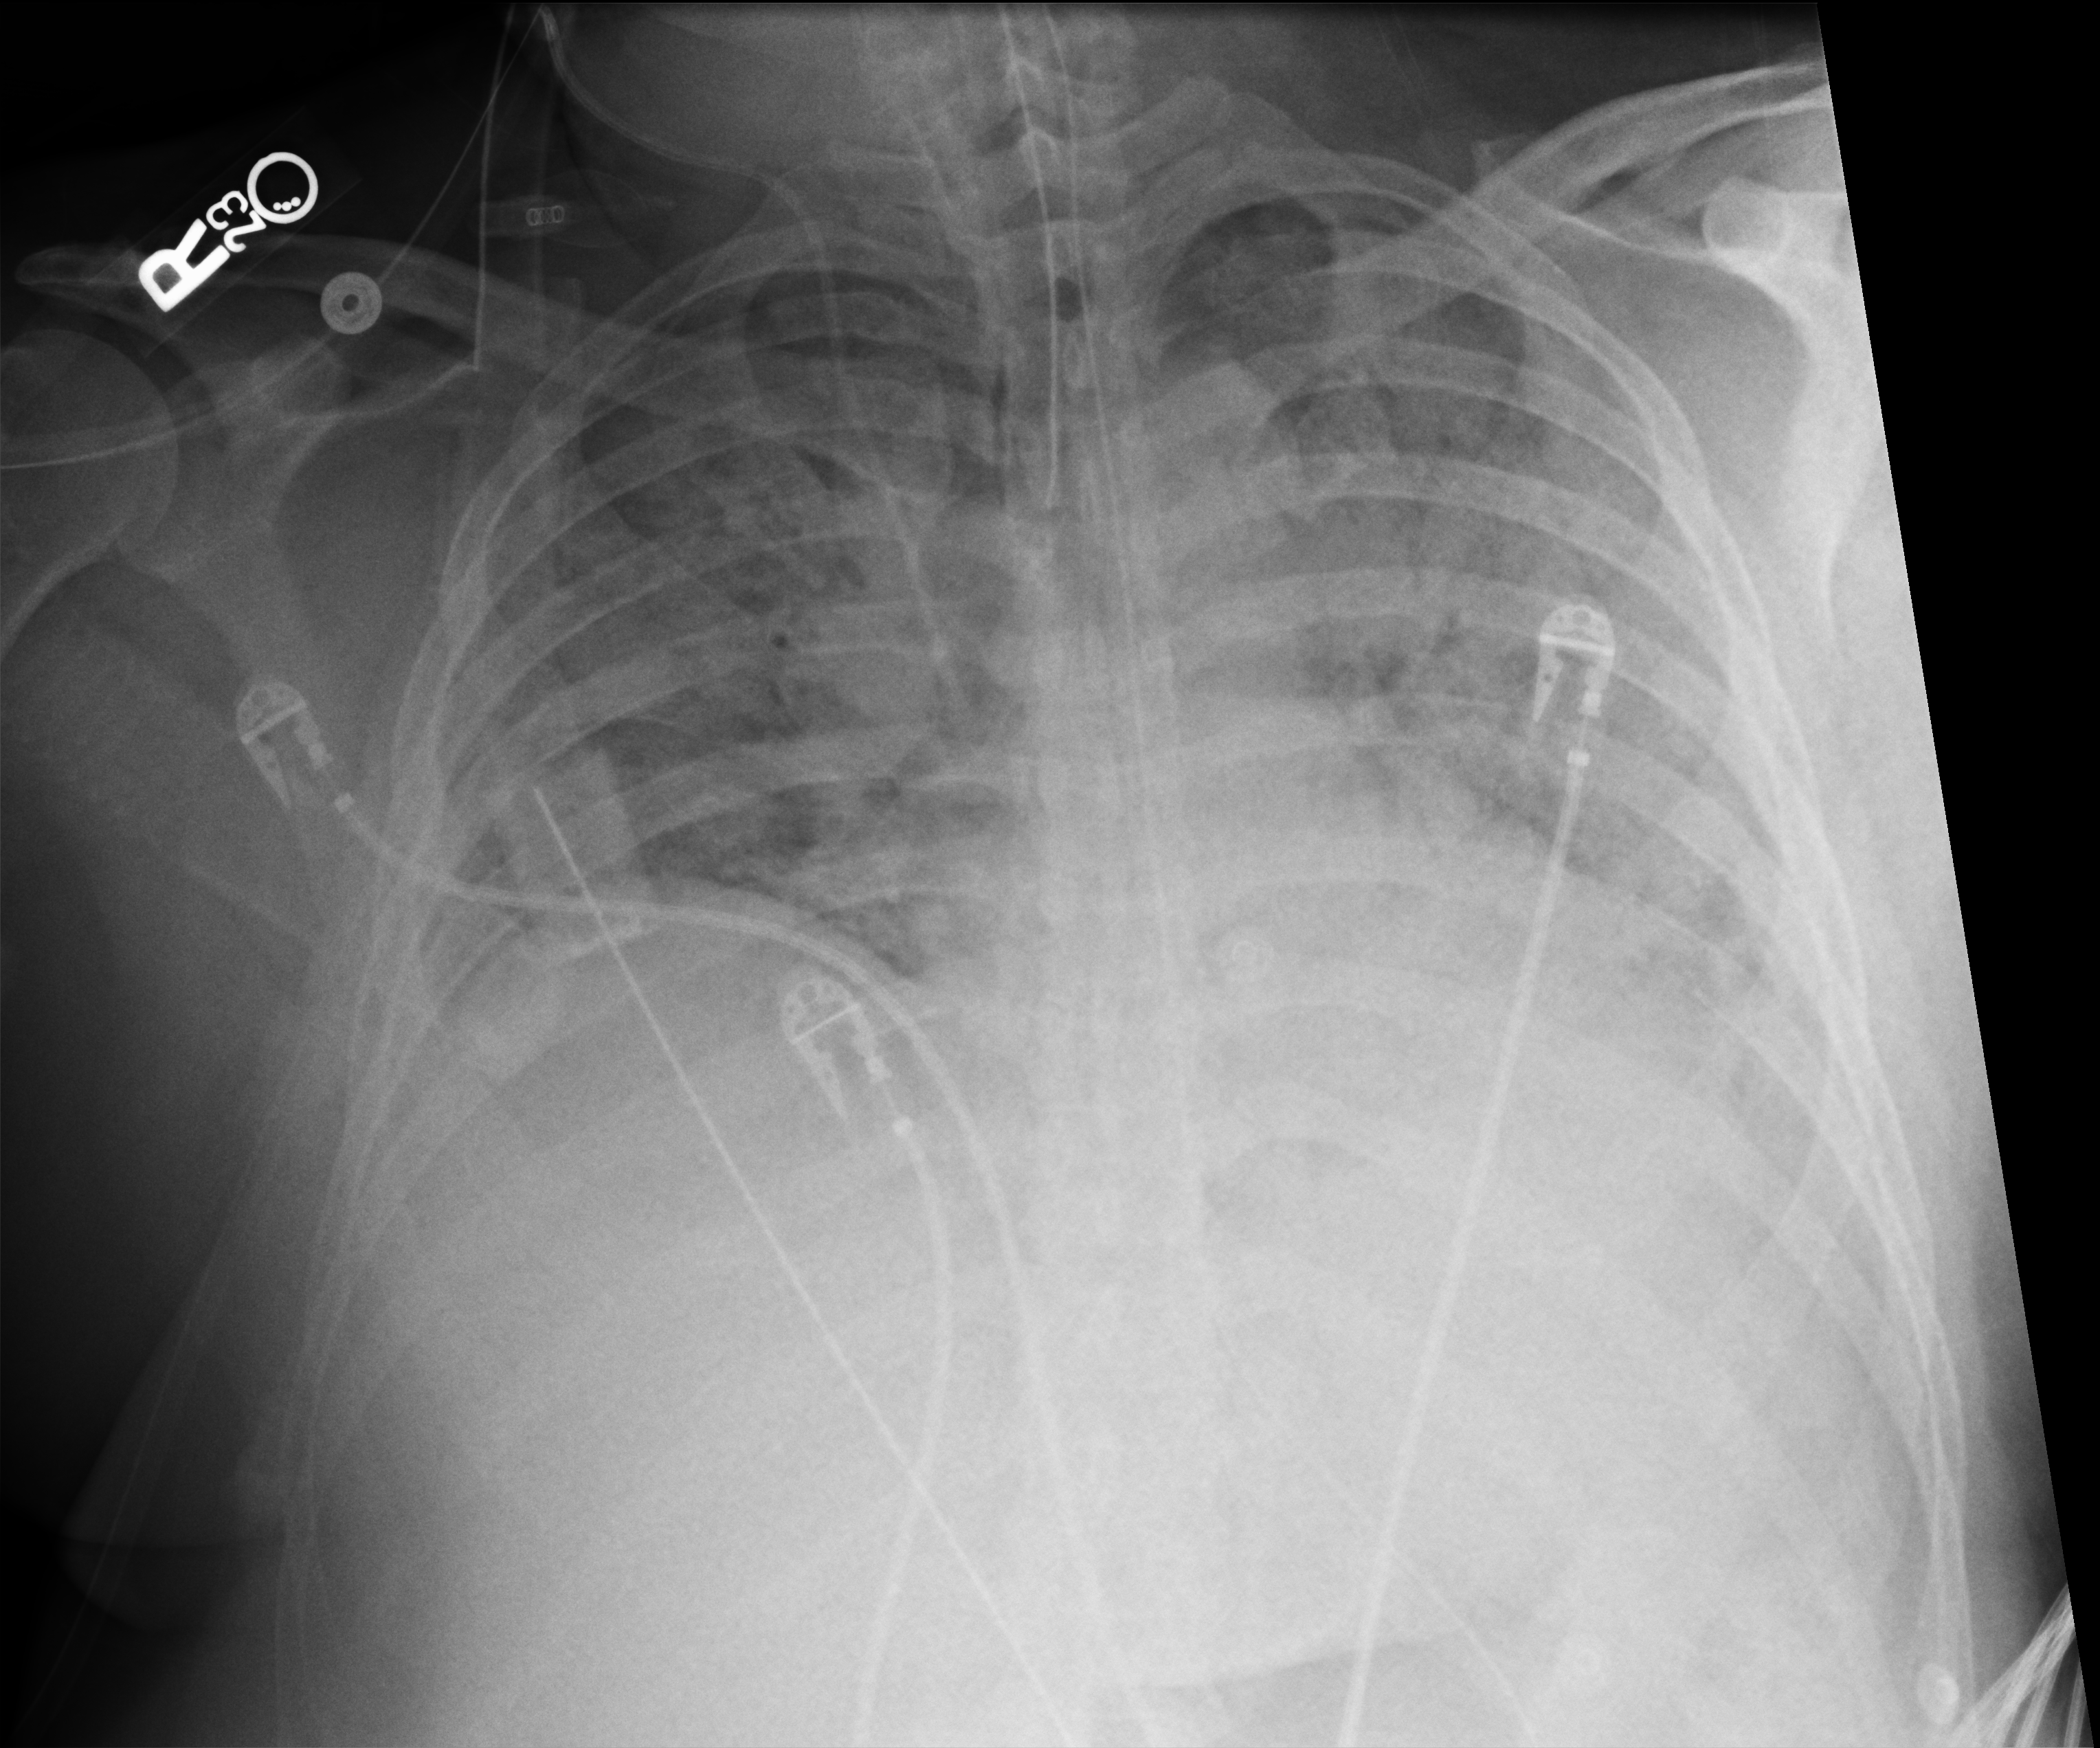
Portable chest radiograph; anteroposterior (AP) projection. Male patient hospitalised with COVID-19, age 18–59 years.
Hospital-stay facts (about this admission, not read from this image; timing relative to this image not recorded):
- mechanically ventilated during this hospital stay: yes